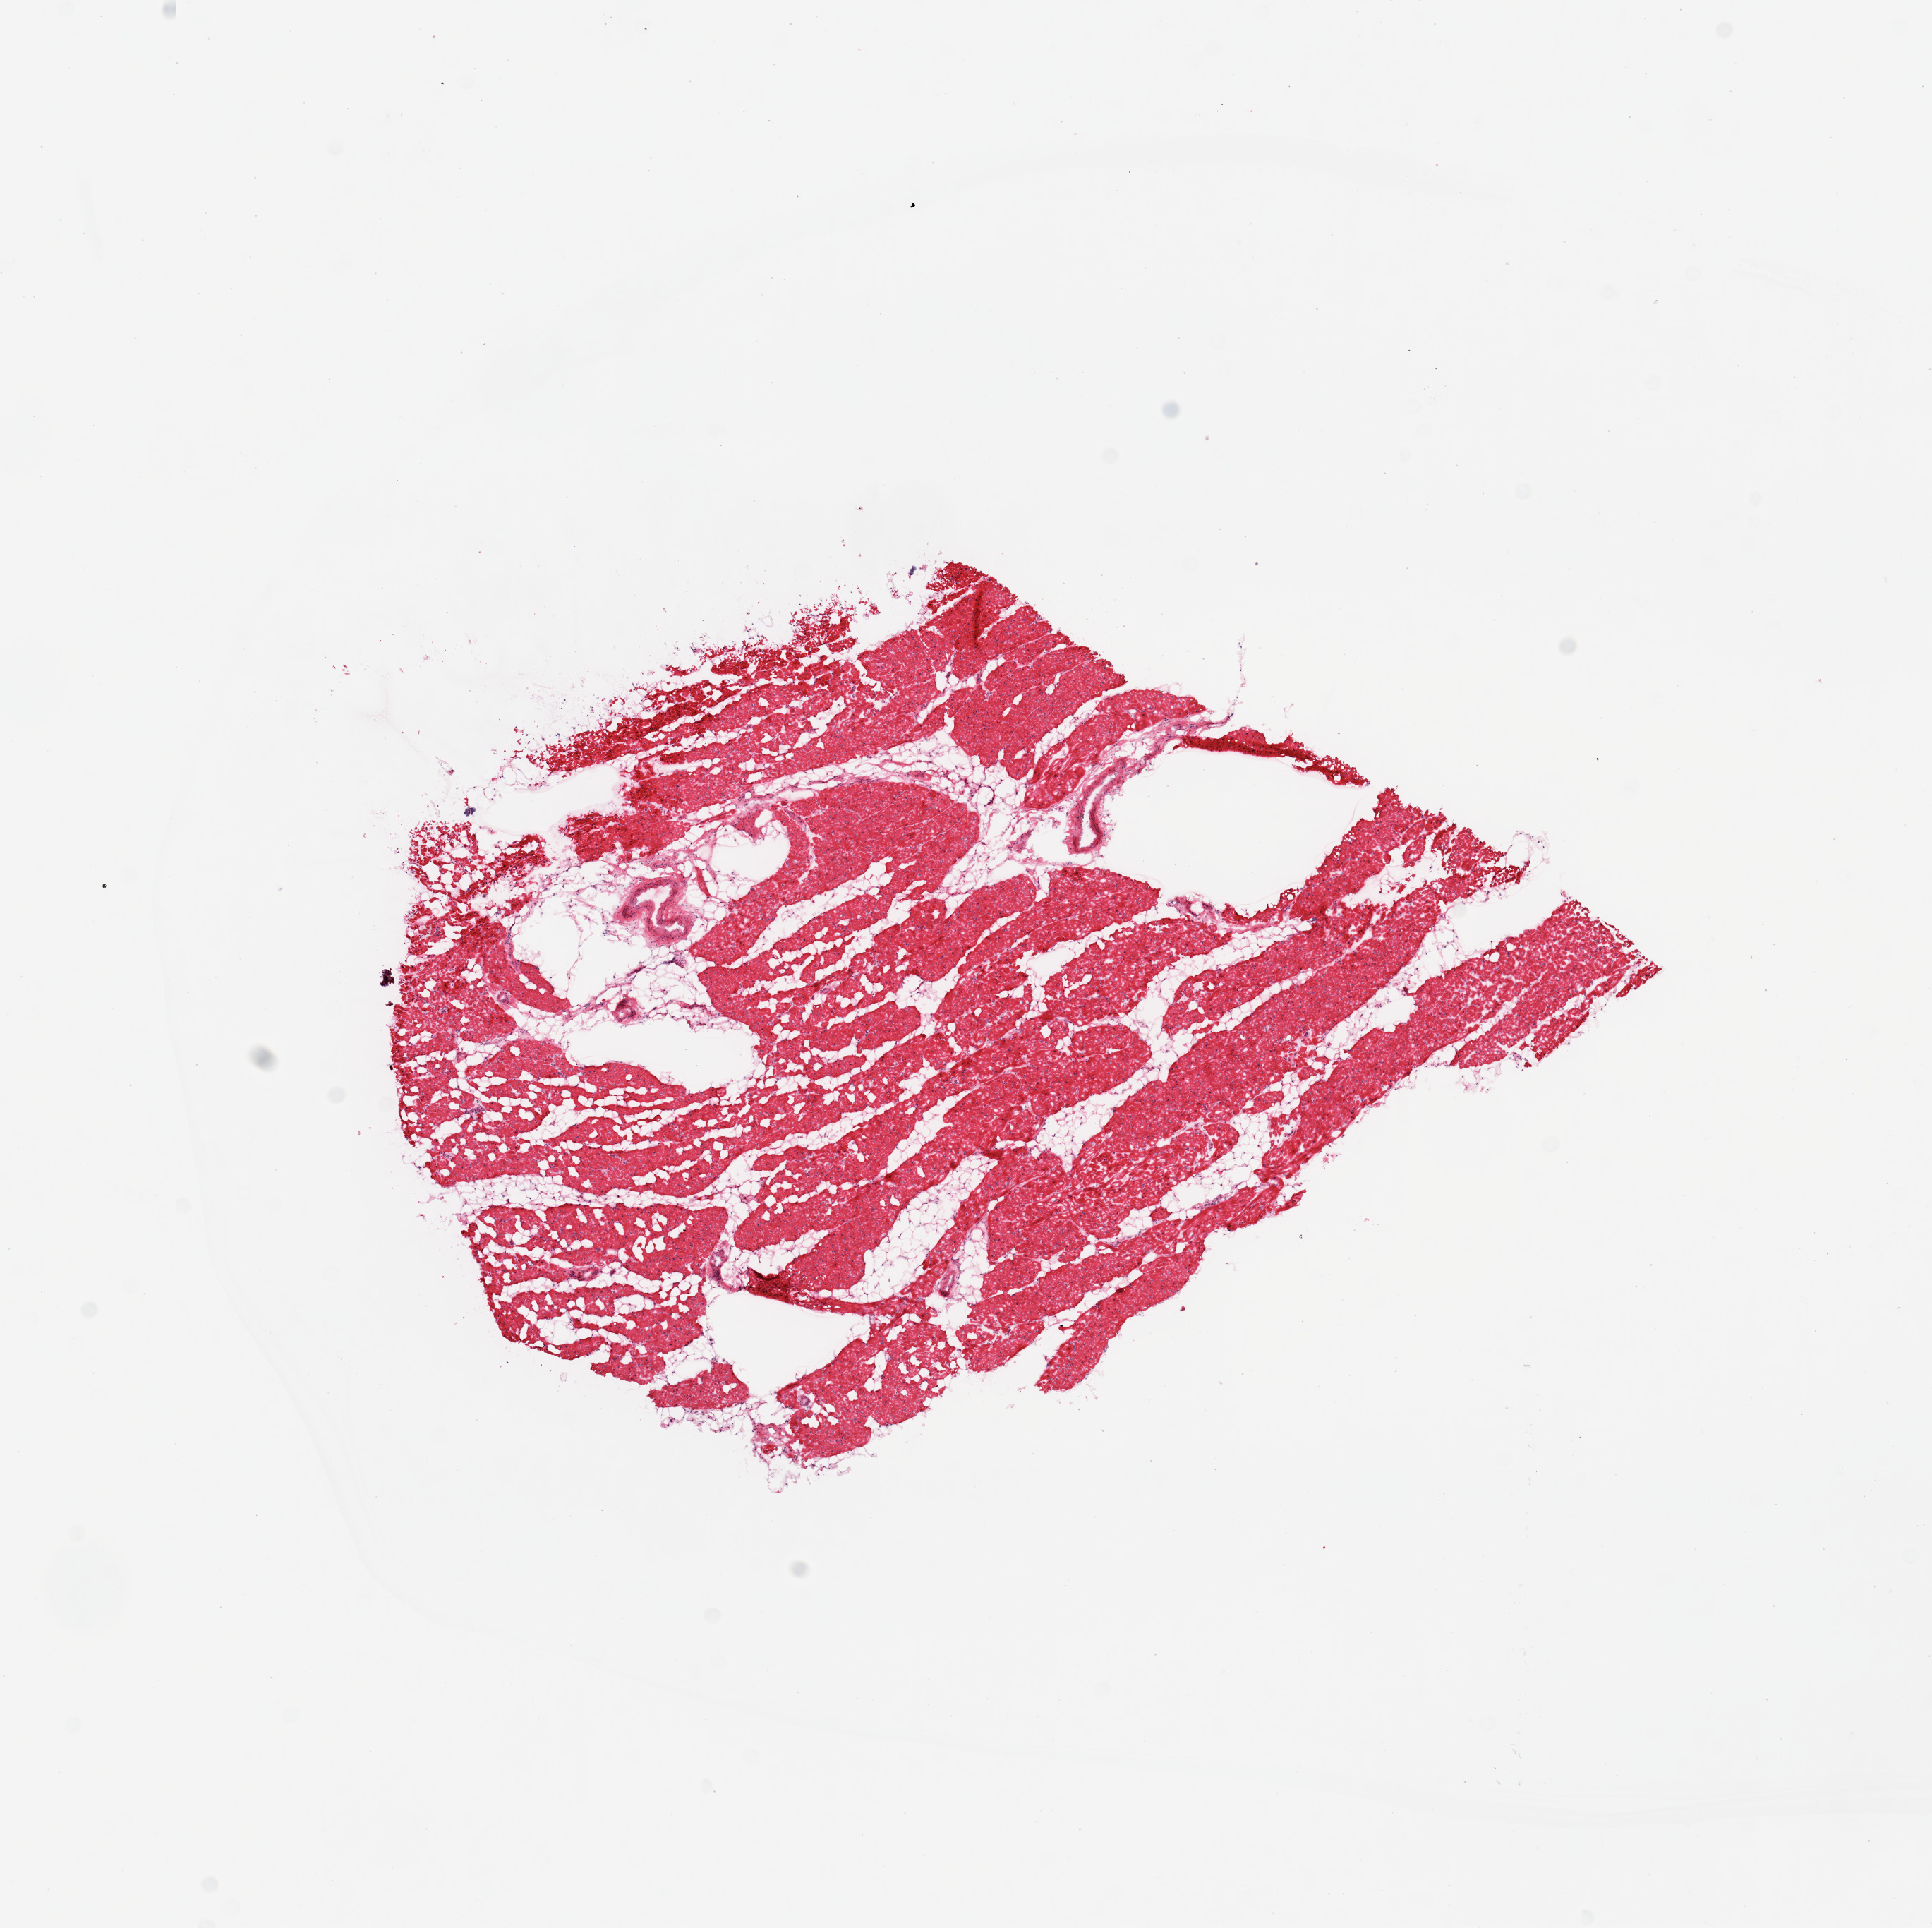
Whole-slide image, H&E stain — whole scanned area (about 10.8 x 10.8 mm, slide scanned at 20x) shown as a low-resolution overview. Donor sex: female.
Specimen: frozen section; sampled site (target tissue): heart; tissue donor sample.